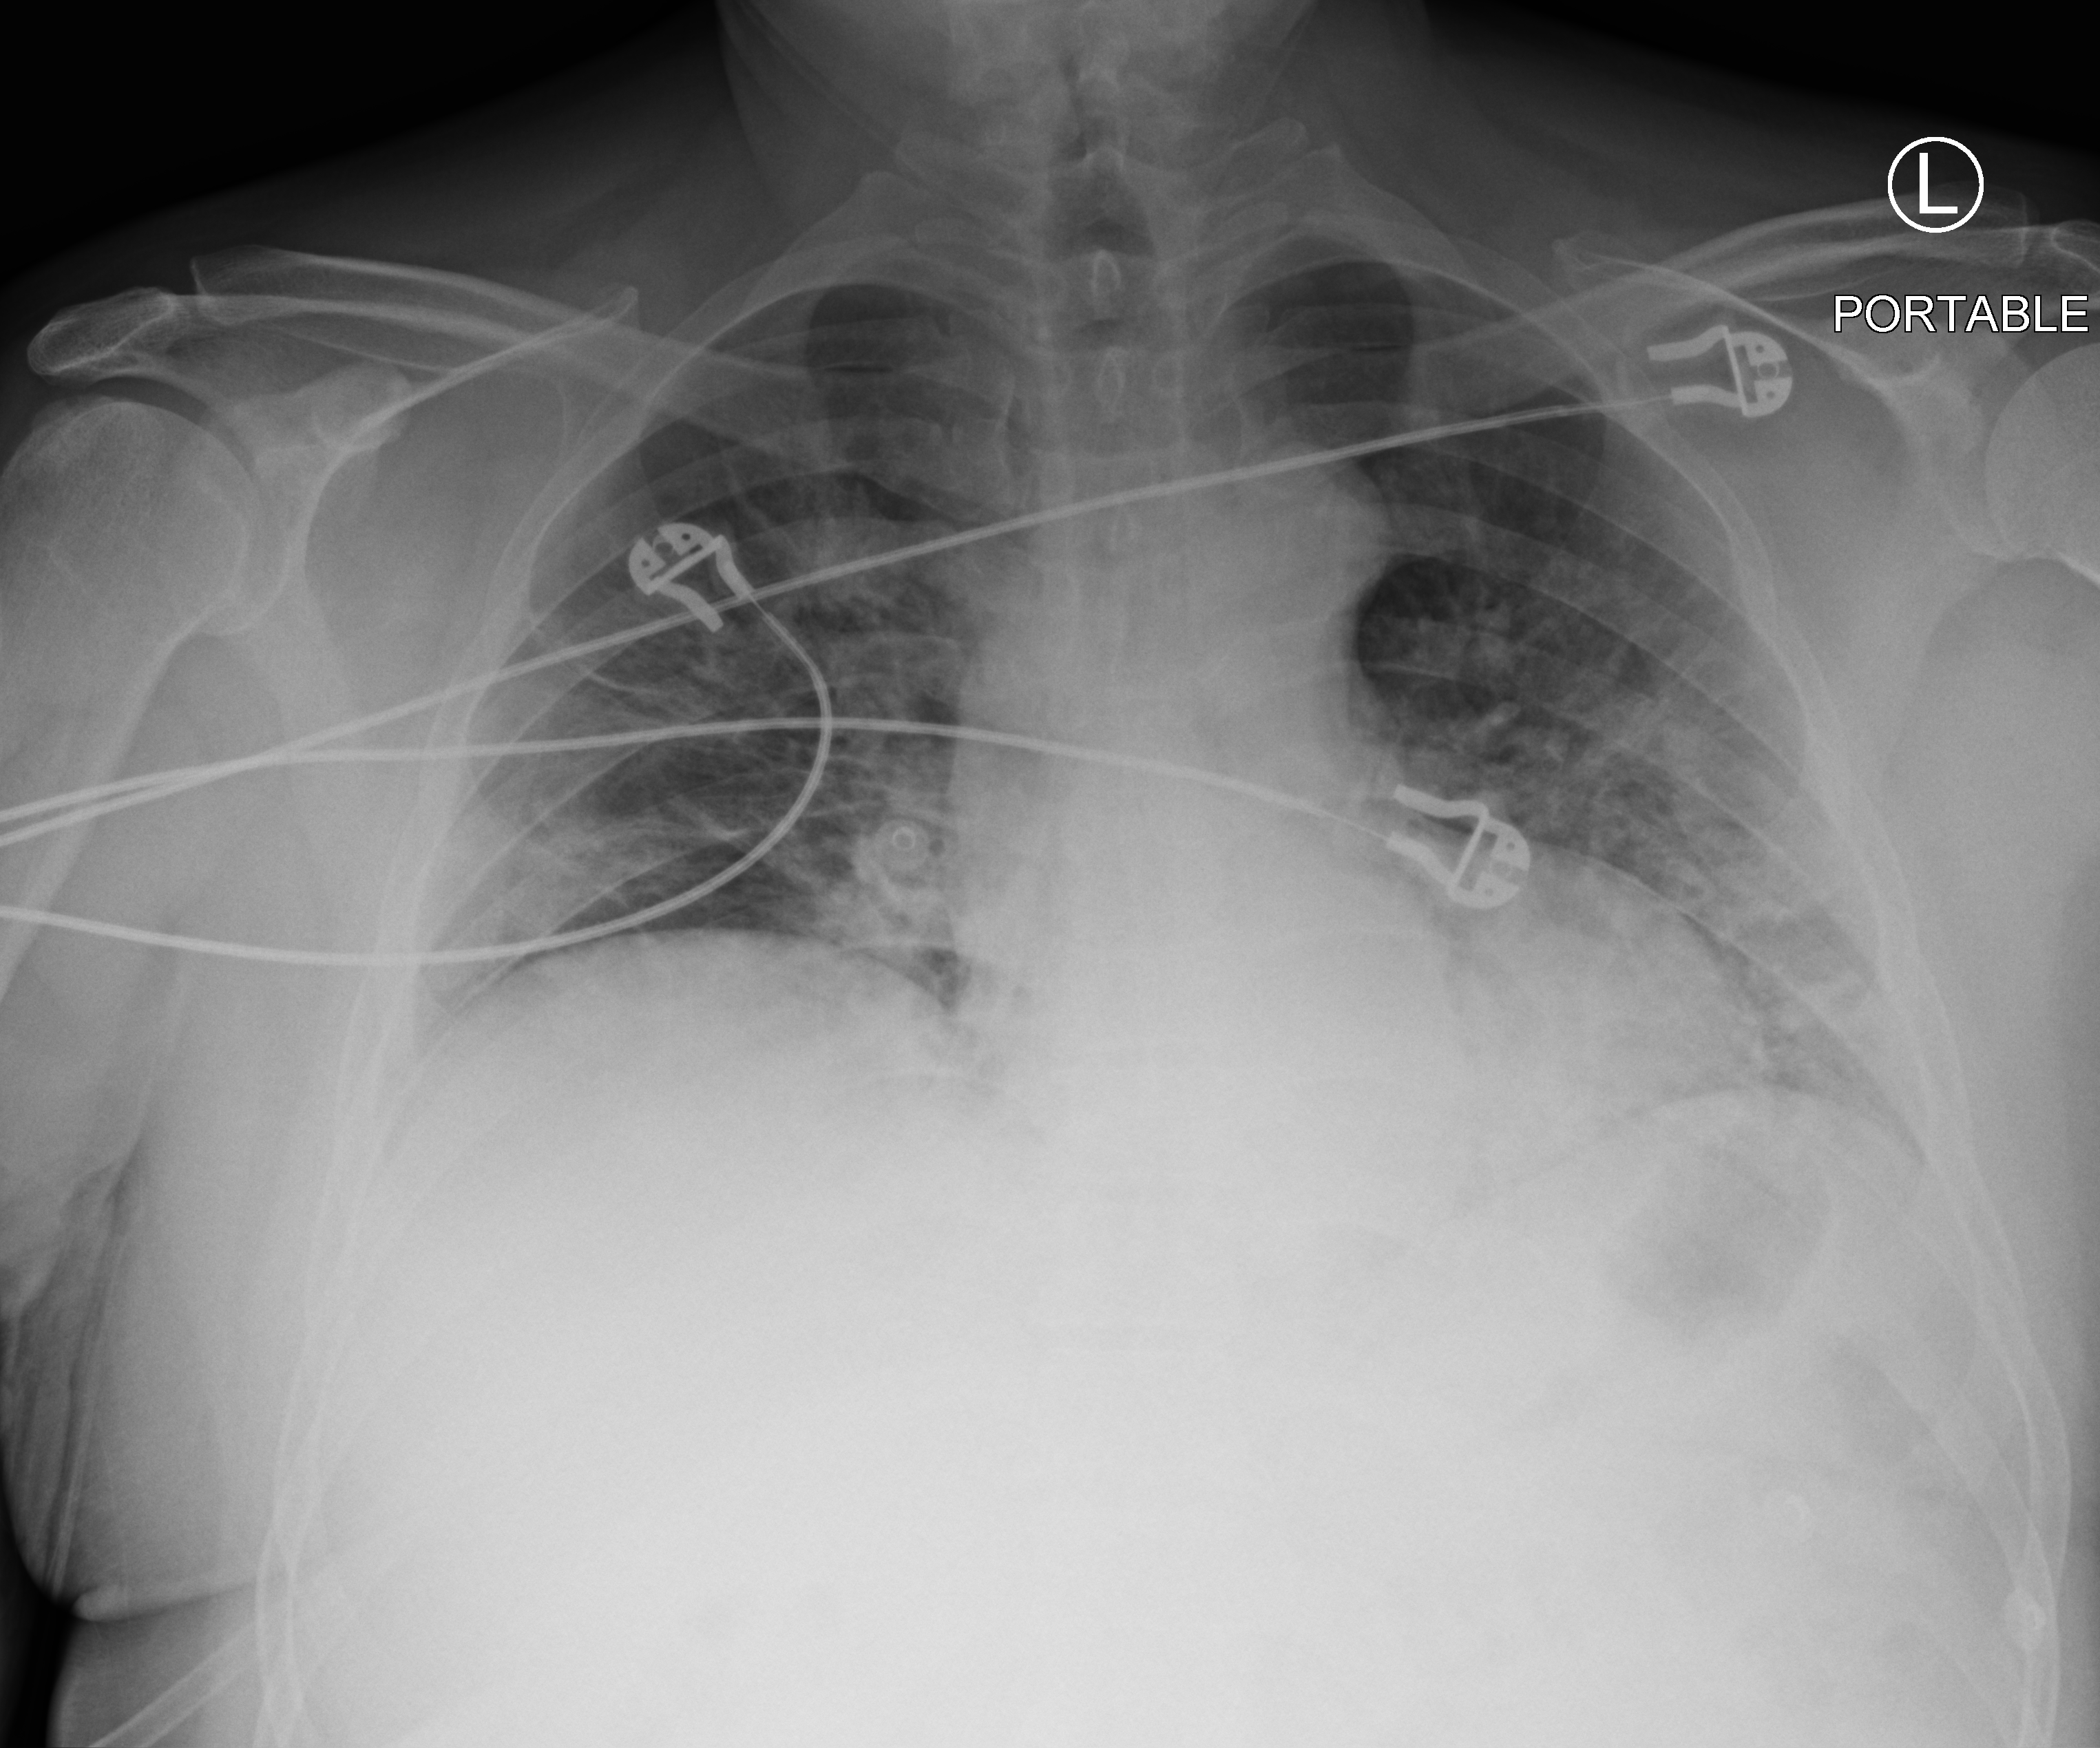
Bedside chest radiograph (computed radiography); anteroposterior (AP) projection. Male patient hospitalised with COVID-19, age 18–59 years.
From the hospital-stay record, not from the radiograph (when in the stay this image was taken is not recorded):
- admitted to intensive care during this hospital stay: no
- diabetes (admission record): yes
- mechanically ventilated during this hospital stay: no